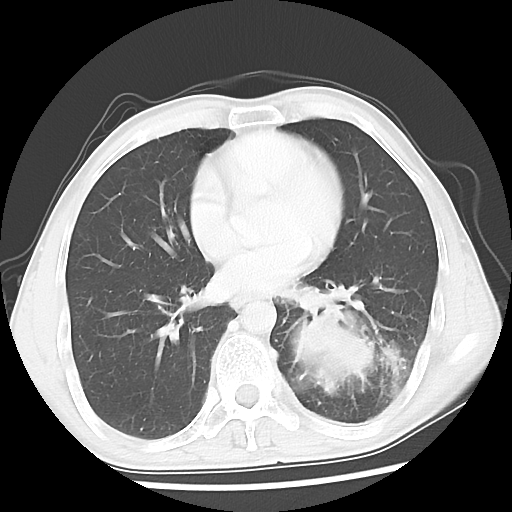
Chest CT, one axial slice. Position 21 of 52 along the scan axis. Reconstruction kernel LUNG. 120 kVp. Lung window (W 1500 / L -600 HU). 512 × 512 image matrix, field of view 318 × 318 mm. Male patient, age 60 years. Case-level facts recorded for this patient, not image findings: clinical TNM (as recorded): T4 N0 M0.
Structures marked on this image (rectangle marked by the reading radiologist):
- lung tumour (recorded histology: squamous cell carcinoma): bounding box [x1, y1, x2, y2] px = [275, 298, 391, 396]